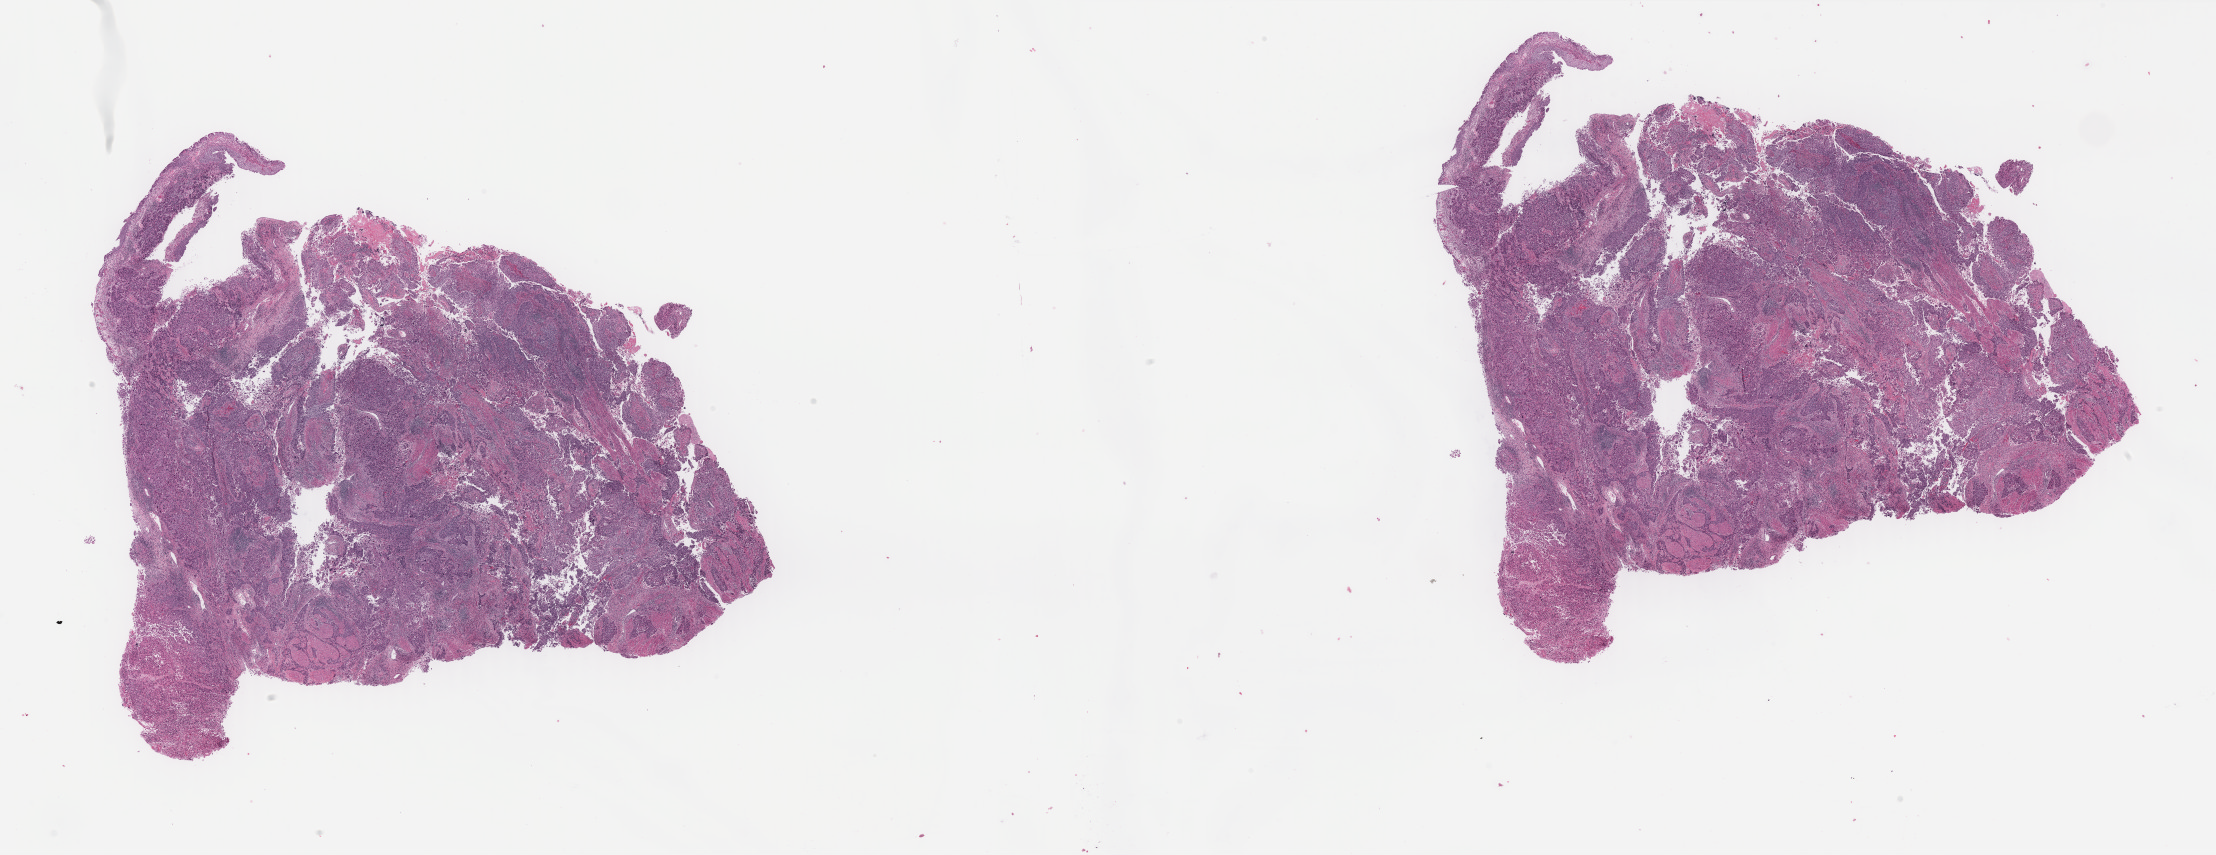
Digitized Hematoxylin and eosin (H&E) stained tissue section (whole slide) — a low-resolution overview of the entire scanned area, about 35.1 x 13.5 mm; formalin-fixed paraffin-embedded (FFPE) diagnostic section; bladder, primary tumour sample. Male patient; age at initial diagnosis 70 years.
Diagnosis: Transitional cell carcinoma.